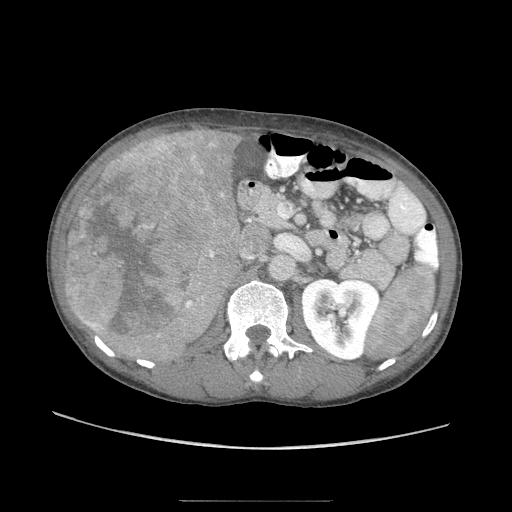
Contrast-enhanced abdominal CT (liver protocol), one axial slice. Position 37 of 103 along the scan axis. Reconstruction kernel STANDARD. Soft-tissue window (W 400 / L 40 HU). 2.5 mm slice thickness. 512 × 512 image matrix. Case-level facts recorded for this patient, not image findings: diagnosis: hepatocellular carcinoma (patient treated with transarterial chemoembolisation; whether this scan precedes or follows treatment is not stated here); TNM stage (as recorded): Stage-IIIA; Child-Pugh class: A; tumour differentiation: moderately differentiated; tumour size: 16 cm.
Outlined on this slice (semi-automatically segmented with operator editing):
- liver parenchyma outside the tumour (the mass and vessels are separate outlines, so this box may not span the whole liver): bounding box <64,126,248,360> (left, top, right, bottom; pixels)
- mass: <64,137,220,345>
- liver vessels: <193,142,213,157>